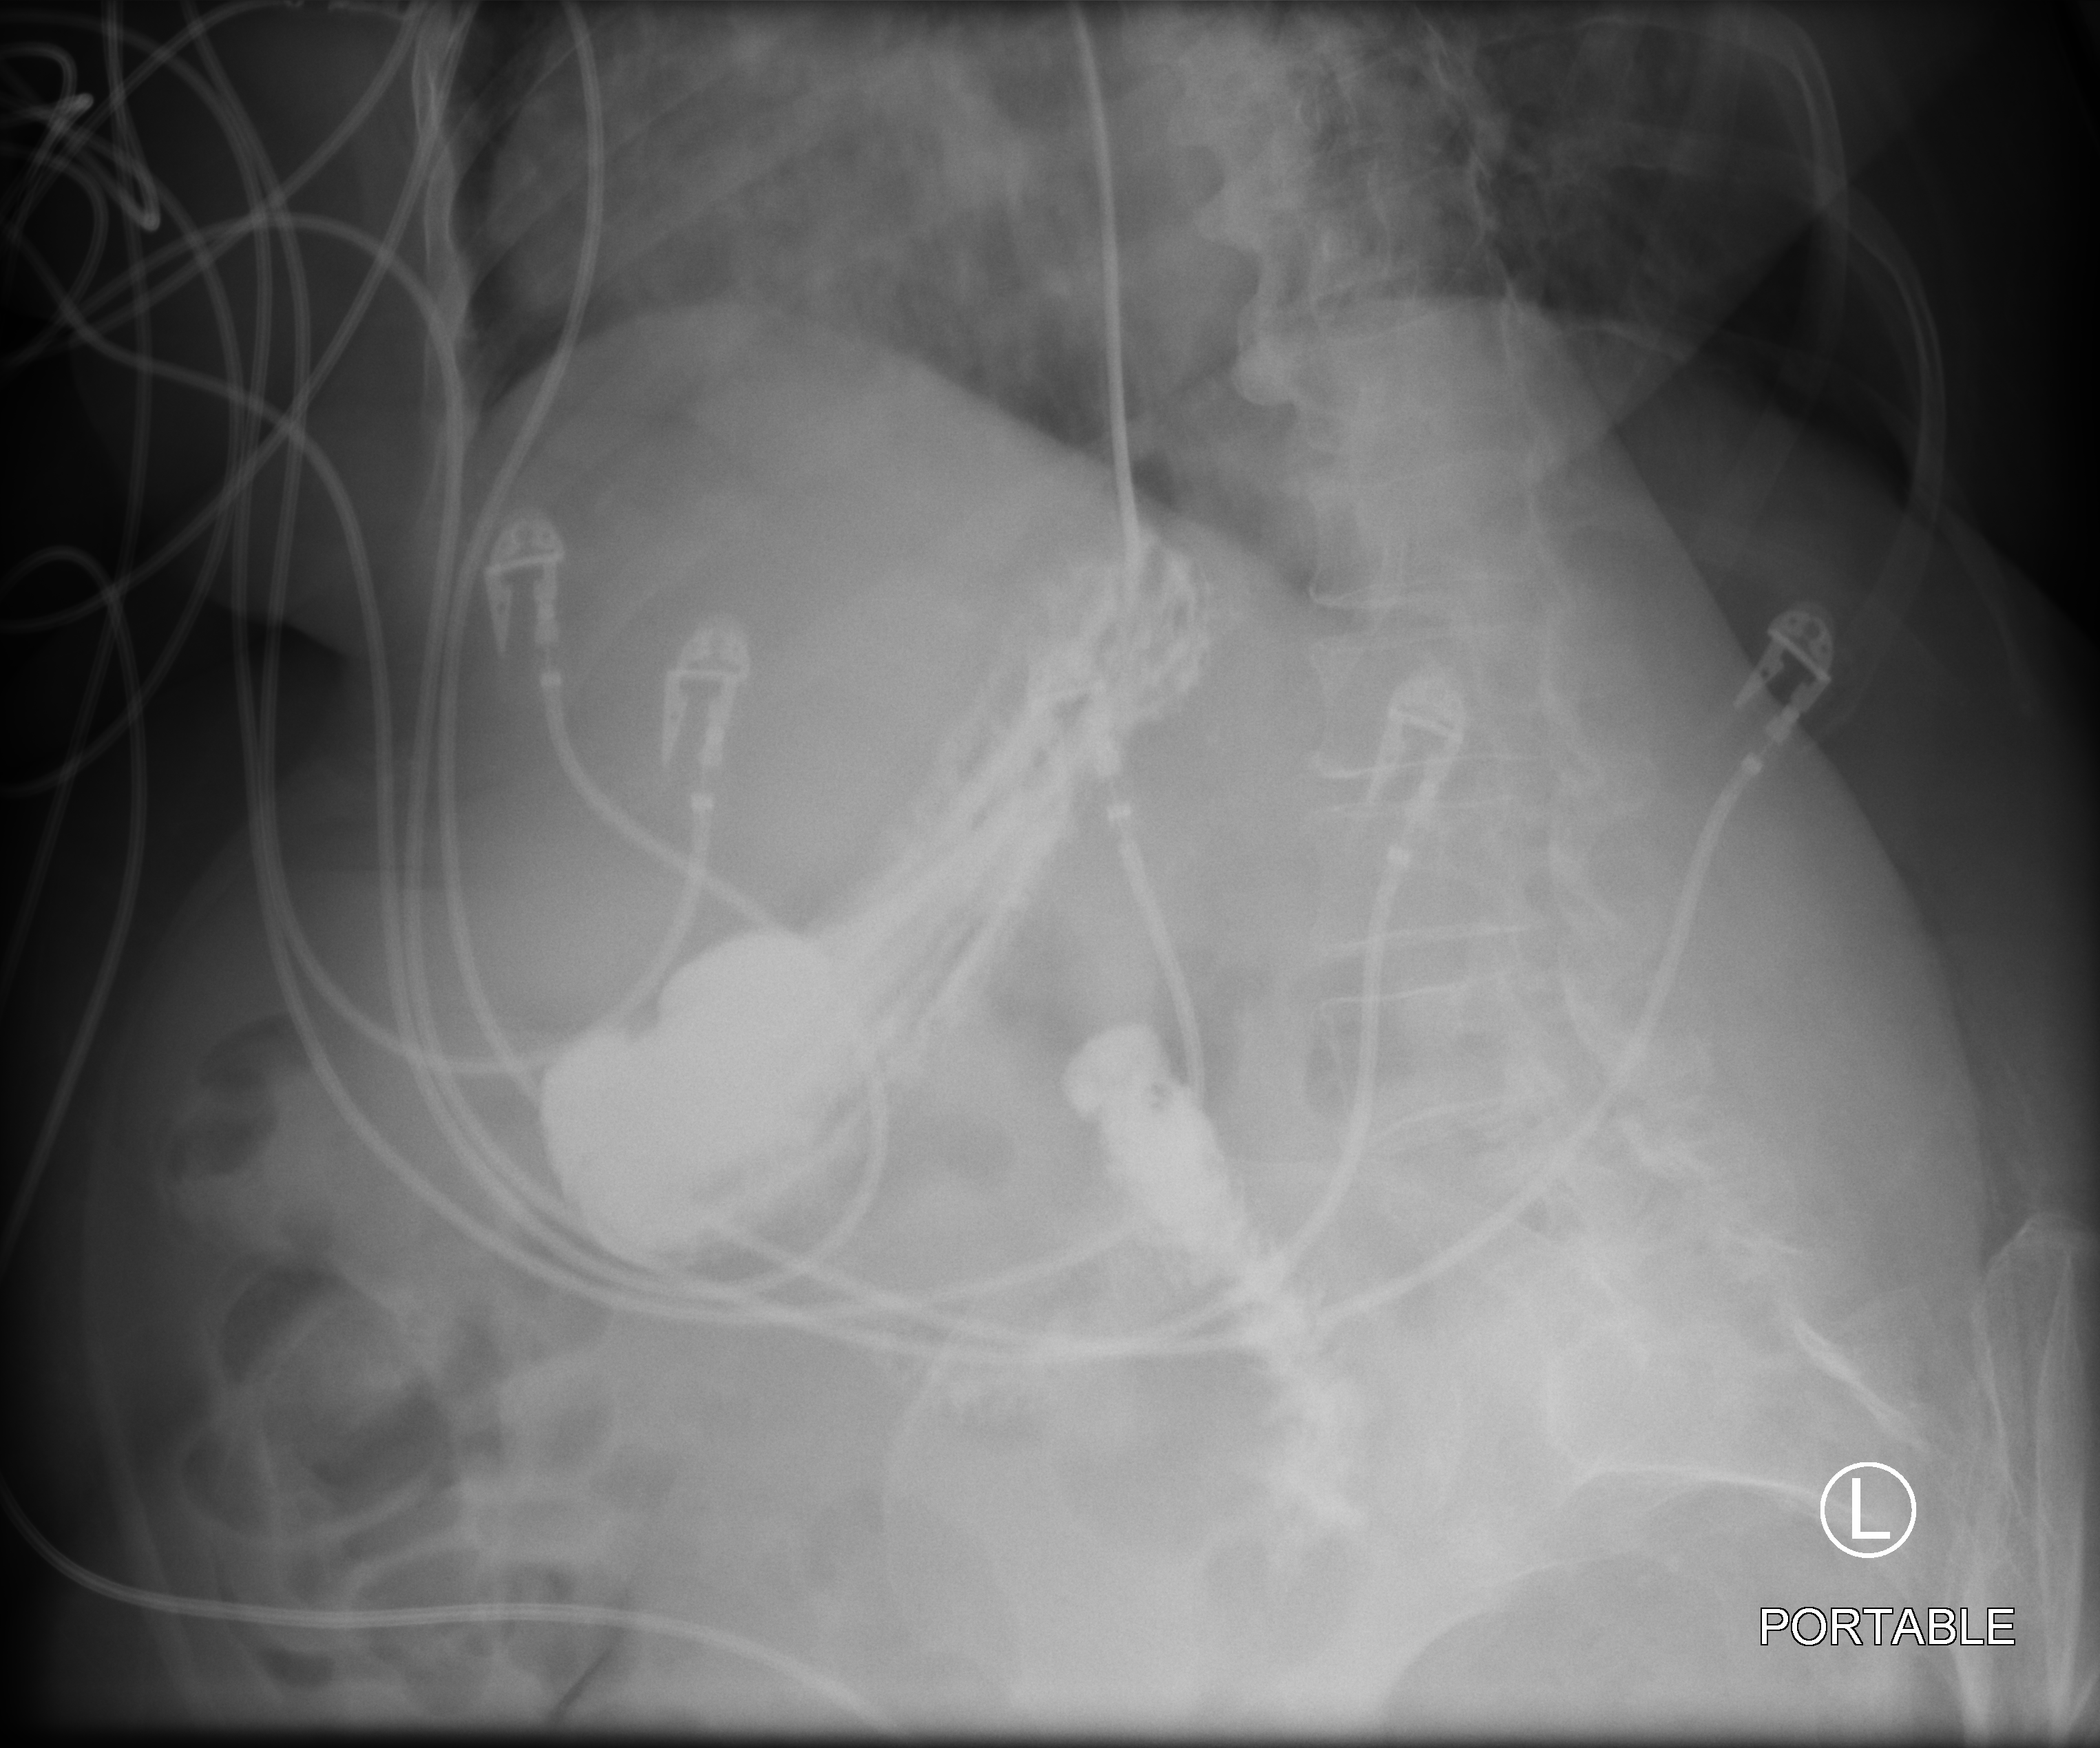
Abdomen X-ray (portable), anteroposterior (AP) projection. Patient hospitalised with COVID-19; female, aged 75–90 years.
From the hospital-stay record, not from the radiograph (when in the stay this image was taken is not recorded):
- mechanically ventilated during this hospital stay: yes
- smoking status (admission record): former
- length of hospital stay: 31 days